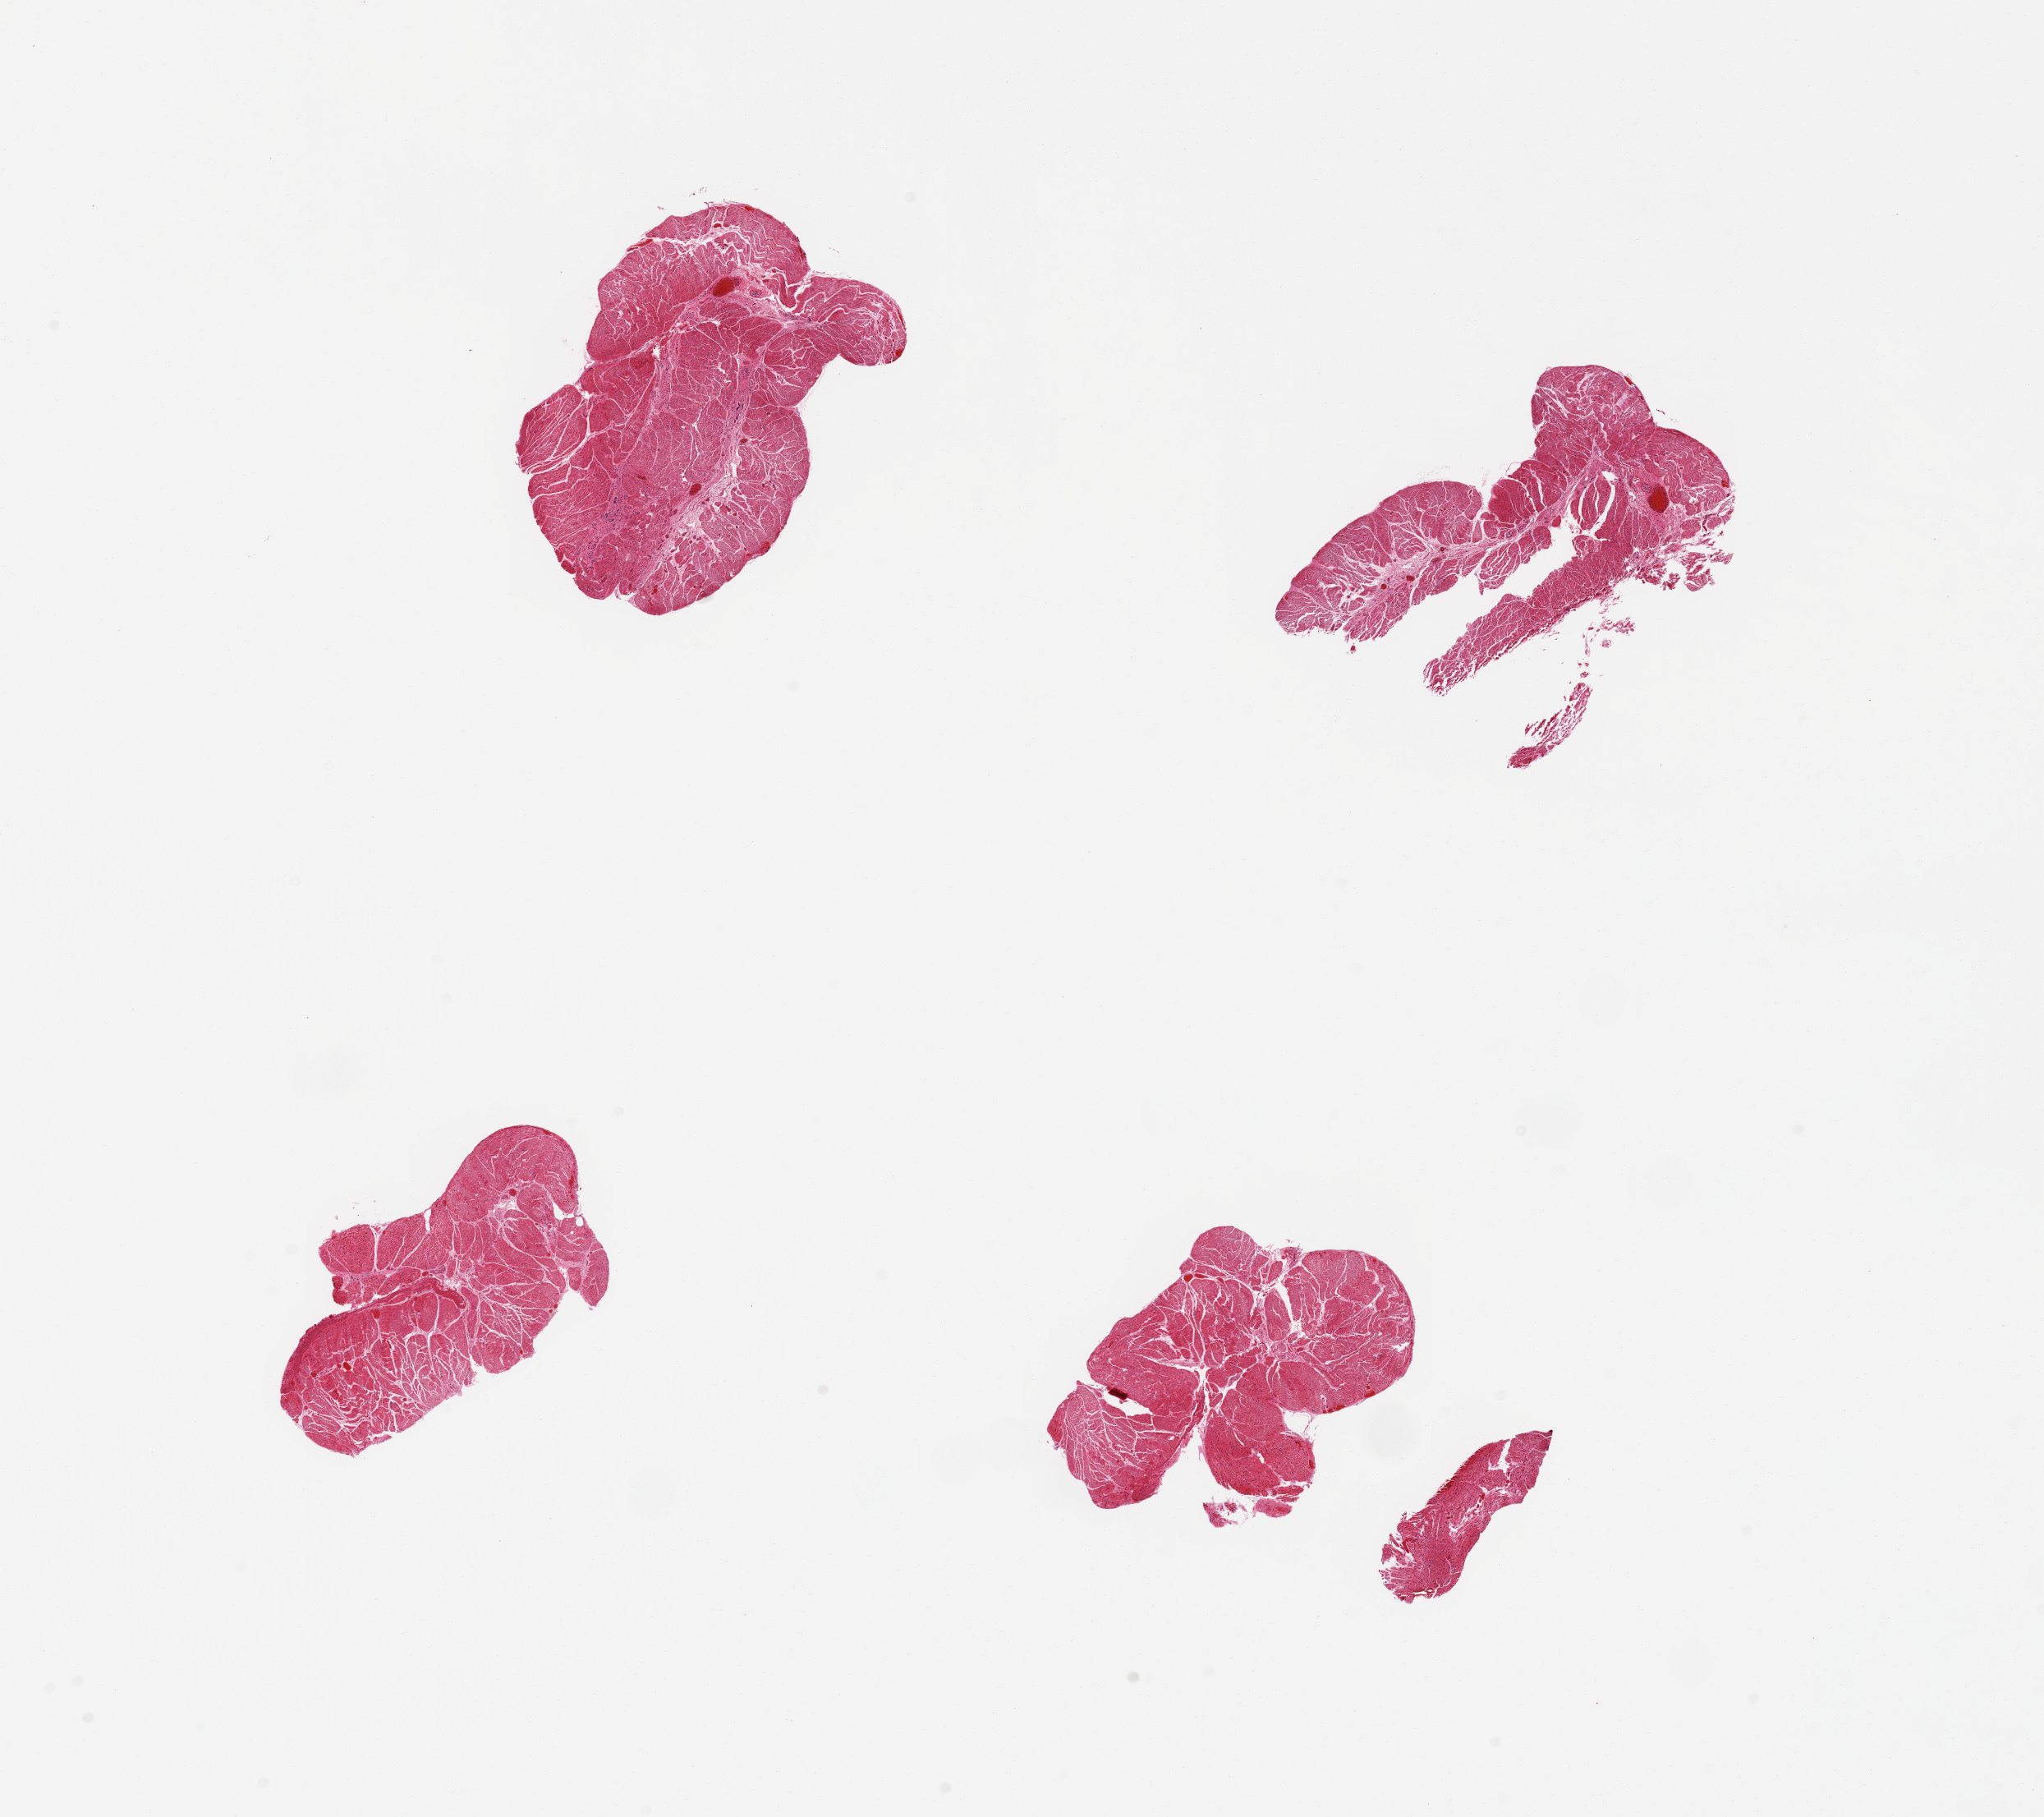
Whole-slide image, haematoxylin and eosin stain, a low-resolution overview of the entire scanned area, about 19.7 x 17.5 mm, PAXgene-fixed, paraffin-embedded tissue, target tissue: esophageal muscle, tissue donor sample. Donor: male.
Reviewer comment on this tissue sample: 4 pieces.